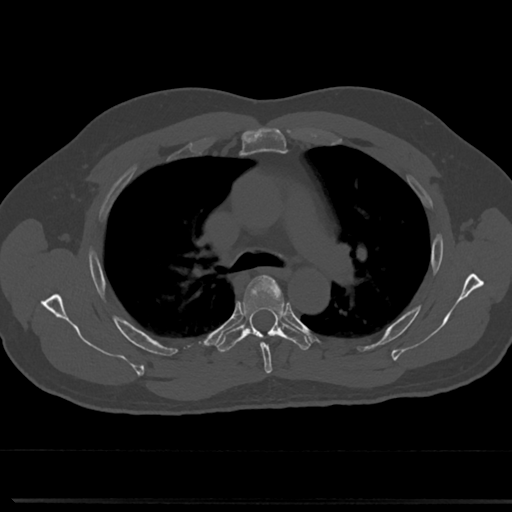
CT including the spine, one axial slice; slice 516 of 817 in the series (ordered by position); reconstruction kernel Br40s/3; 120 kVp; bone window (W 1800 / L 400 HU); 0.5 mm slice thickness; 512 × 512 image matrix, field of view 355 × 355 mm. Patient: male, 61 years. Case-level facts recorded for this patient, not image findings: primary cancer: prostate.
Outlined on this slice (semi-automatically segmented with operator editing):
- T4 vertebra: bounding box (x1, y1, x2, y2) in pixels: (241, 275, 288, 364)
- T5 vertebra: (220, 306, 310, 350)